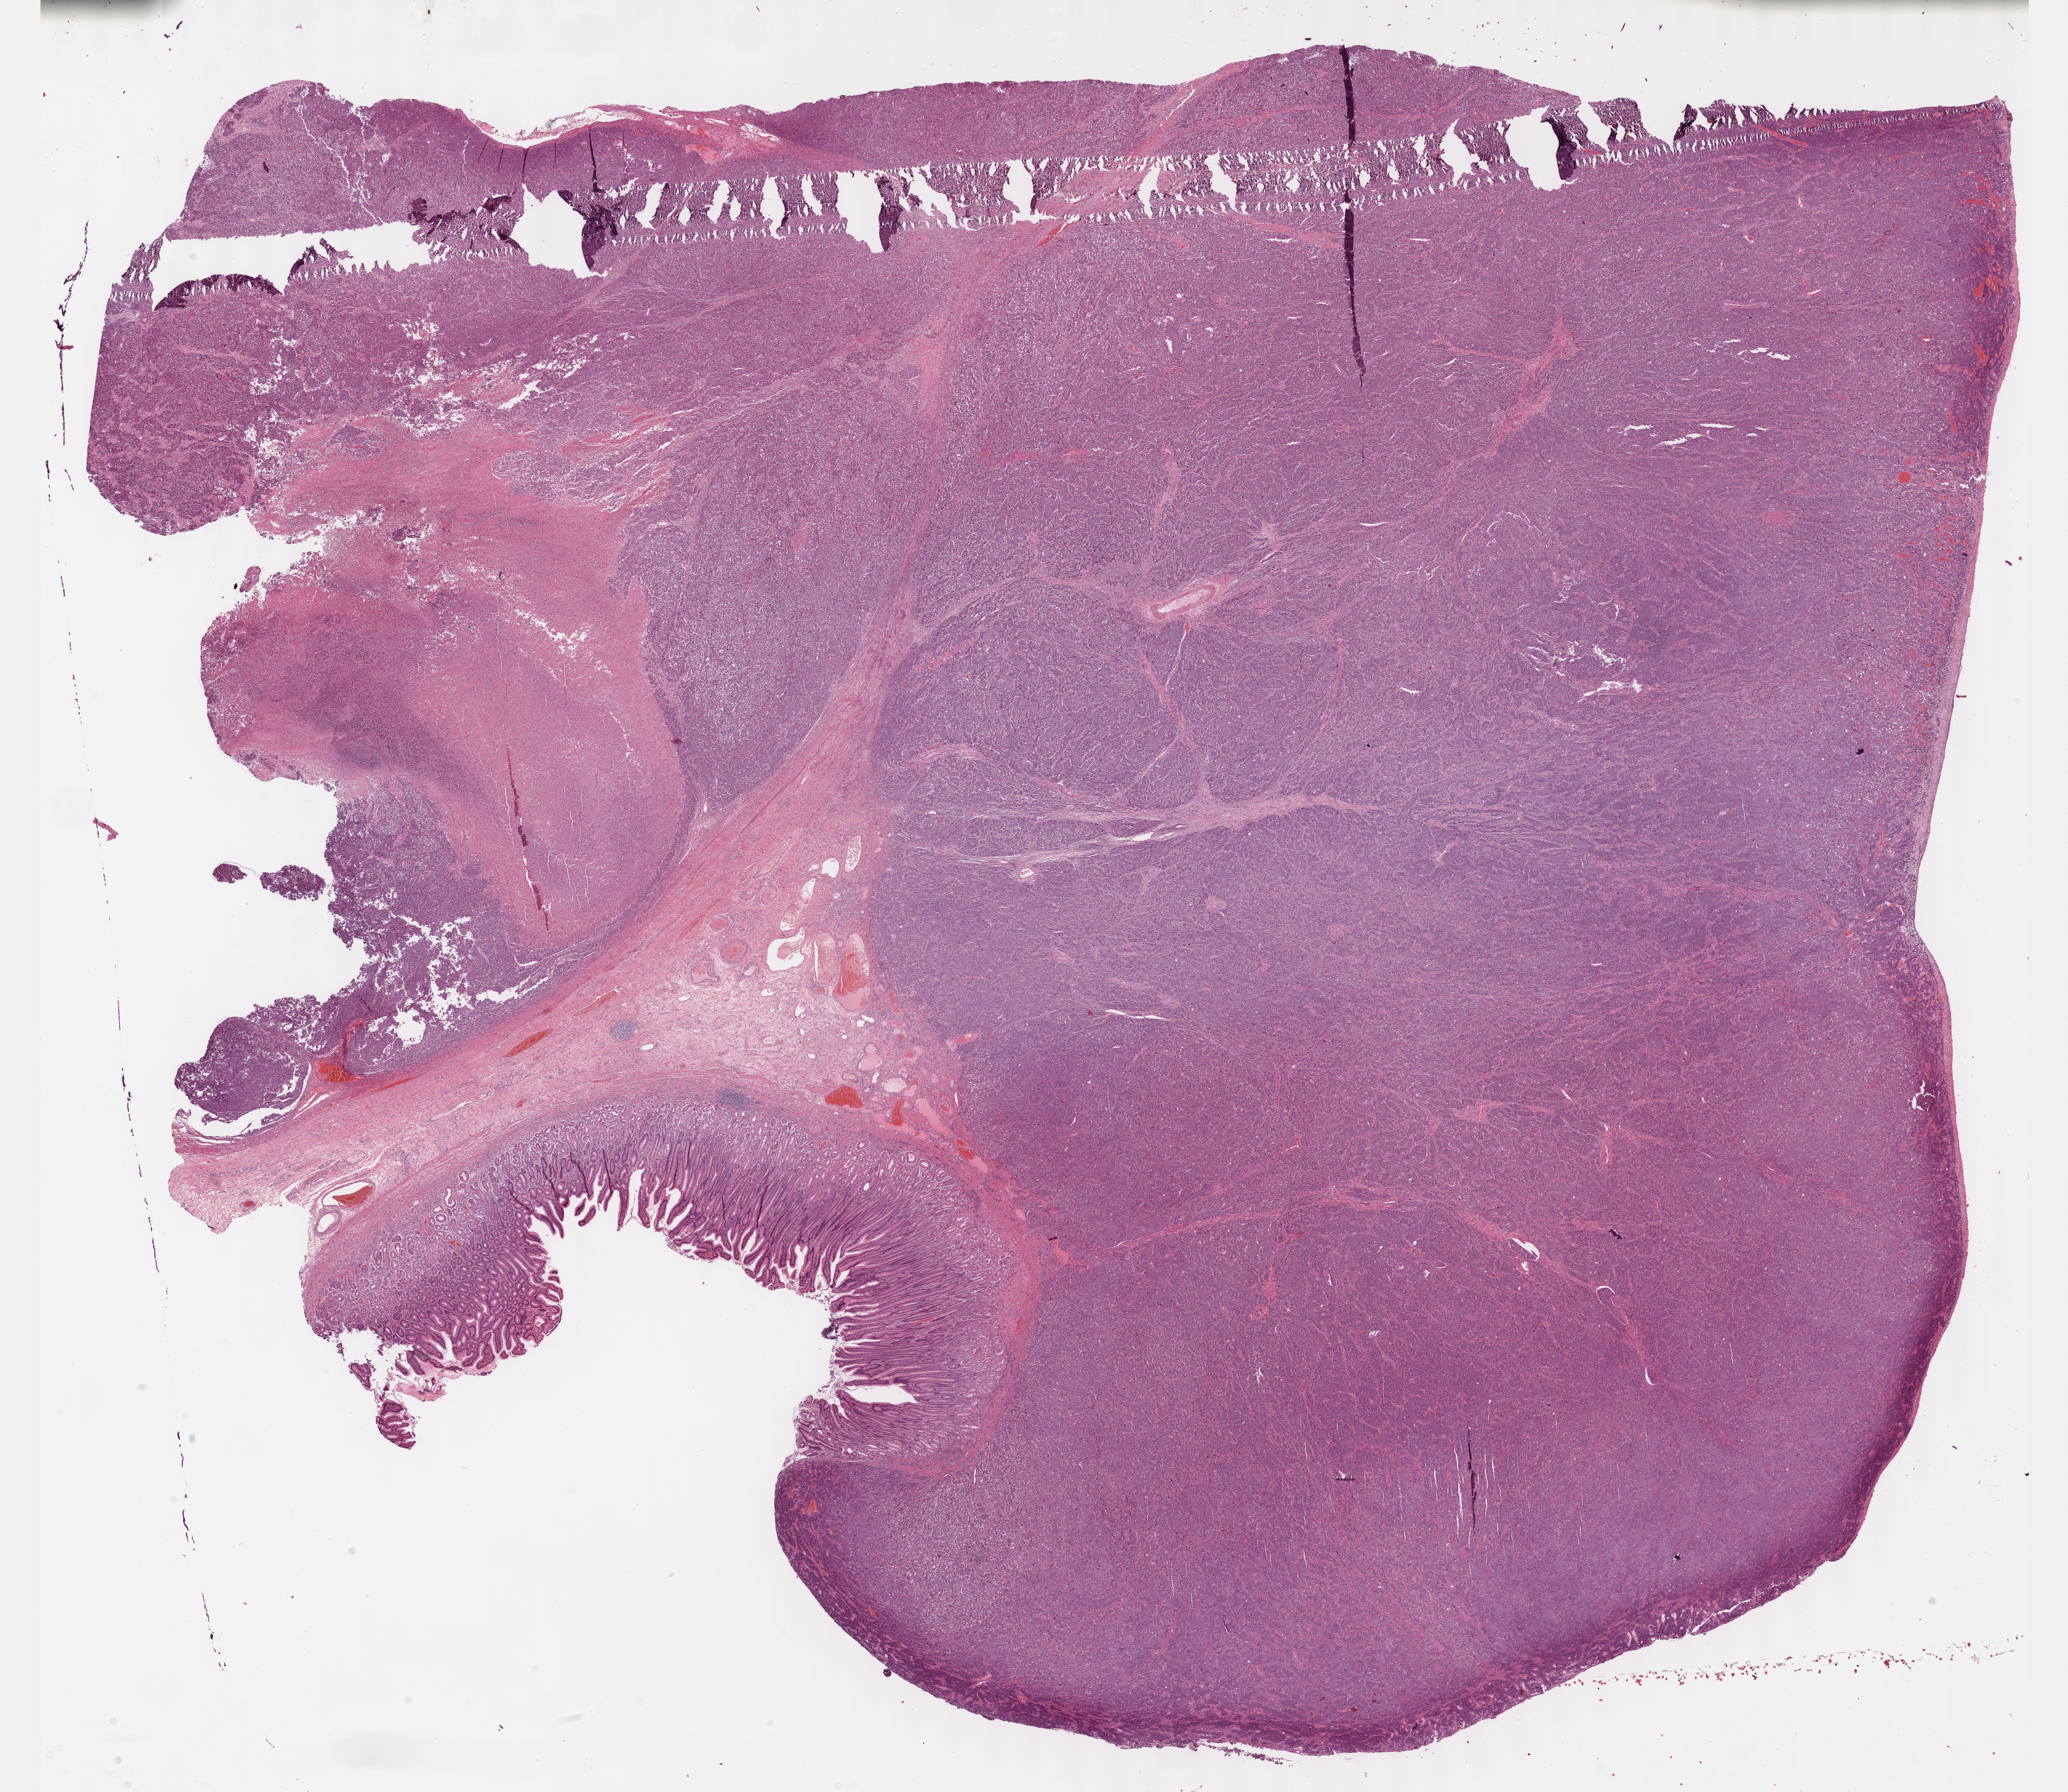
Hematoxylin and eosin (H&E) stained whole-slide image — whole scanned area (about 25.7 x 22.2 mm) shown as a low-resolution overview; formalin-fixed paraffin-embedded (FFPE) diagnostic section; stomach, primary tumour sample. Patient: male, age at initial diagnosis 65 years. Histologic grade: G3 (poorly differentiated).
- lymph nodes positive (case pathology): 0 of 38 examined
- pathologic diagnosis: Adenocarcinoma, intestinal type (body of stomach)
- TNM: T4b N0 M0
- AJCC pathologic stage: IIIB (7th edition)